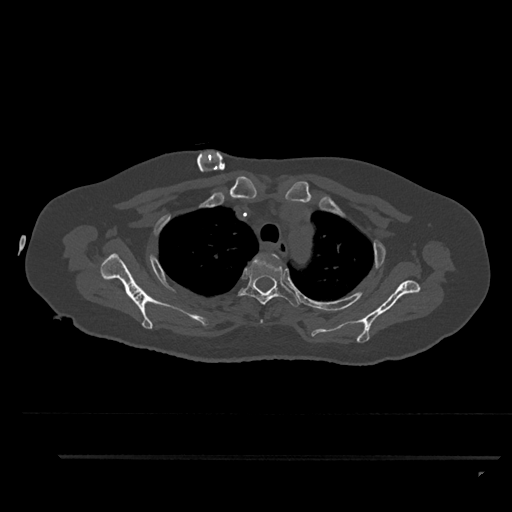
CT including the spine, one axial slice. Reconstruction kernel Br40s/3. 120 kVp. Bone window (W 1800 / L 400 HU). 512 × 512 image matrix. Patient: female, 44 years. Case-level facts recorded for this patient, not image findings: primary cancer: renal.
Annotated regions visible in this slice (semi-automatic segmentation, software-assisted and operator-edited):
- T2 vertebra: bounding box <260,253,281,324> (left, top, right, bottom; pixels)
- T3 vertebra: <237,255,301,307>